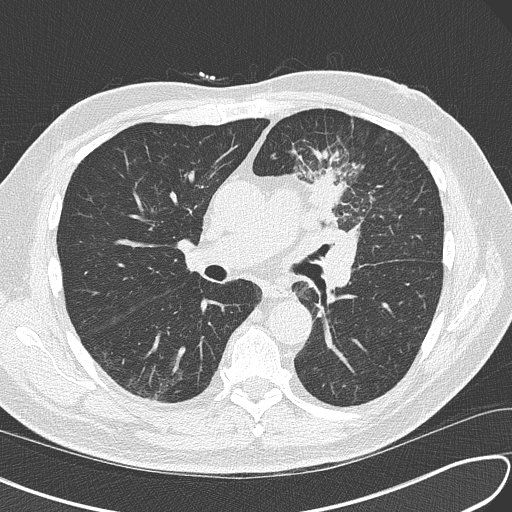
Chest CT (low-dose screening protocol), one axial image, third screening round (two years after baseline), lung window (W 1500 / L -600 HU), 2 mm slice thickness, lung (sharp) reconstruction kernel (B50f), slice 69 of 156 in the series. Male, age 67 years at enrolment.
Expert reader's lesion annotation, bounding box <293,156,393,244> (left, top, right, bottom; pixels). Screening reader's record for this exam (one nodule recorded; not confirmed to be the boxed lesion): non-calcified nodule or mass ≥4 mm, left upper lobe, 30 × 23 mm, soft tissue attenuation, pre-existing on the prior screen: no. Lung cancer was diagnosed 41 days after this screen: small cell carcinoma, NOS, left upper lobe, stage IV (AJCC 6th edition), 30 mm at pathology.